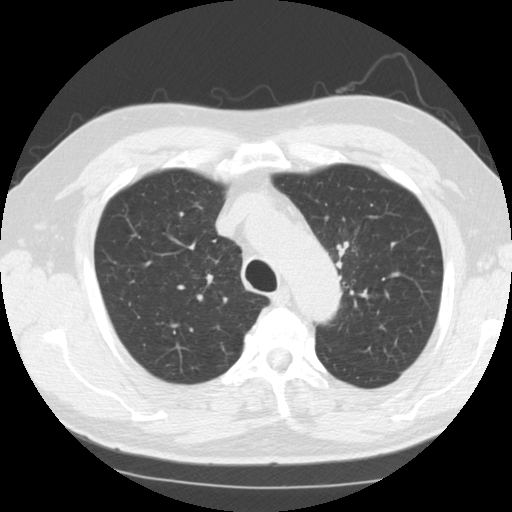
Axial slice from a low-dose chest CT screening exam; third annual screen; lung window (W 1500 / L -600 HU); 2.5 mm slice thickness; 120 kVp; slice 28 of 124 in the series. Male, age 60 years at enrolment.
• Expert-annotated lung lesion, bounding box [x1, y1, x2, y2] px = [319, 230, 372, 295].
• The exam's reader record, not a measurement of the box and not confirmed to be the same lesion: non-calcified nodule or mass ≥4 mm, left upper lobe, 24 × 21 mm, smooth margins, soft tissue attenuation, pre-existing on the prior screen: no.
• Official screen result: positive, other.
• Participant outcome: lung cancer diagnosed 14 days after this screen — small cell carcinoma, NOS, left upper lobe, stage IIA (AJCC 6th edition), 26 mm at pathology.